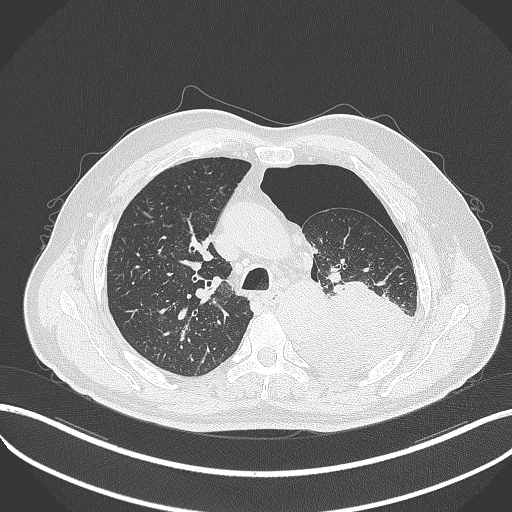
Chest CT, one axial slice; position 357 of 464 along the scan axis; lung window (W 1500 / L -600 HU); 1 mm slice thickness; 512 × 512 image matrix. Male patient, age 76 years. From the clinical record (not read from this slice): clinical TNM (as recorded): T3 N0 M1b.
Annotated regions visible in this slice (rectangle marked by the reading radiologist):
- lung tumour (recorded histology: adenocarcinoma): bounding box (x1, y1, x2, y2) in pixels: (301, 277, 417, 378)